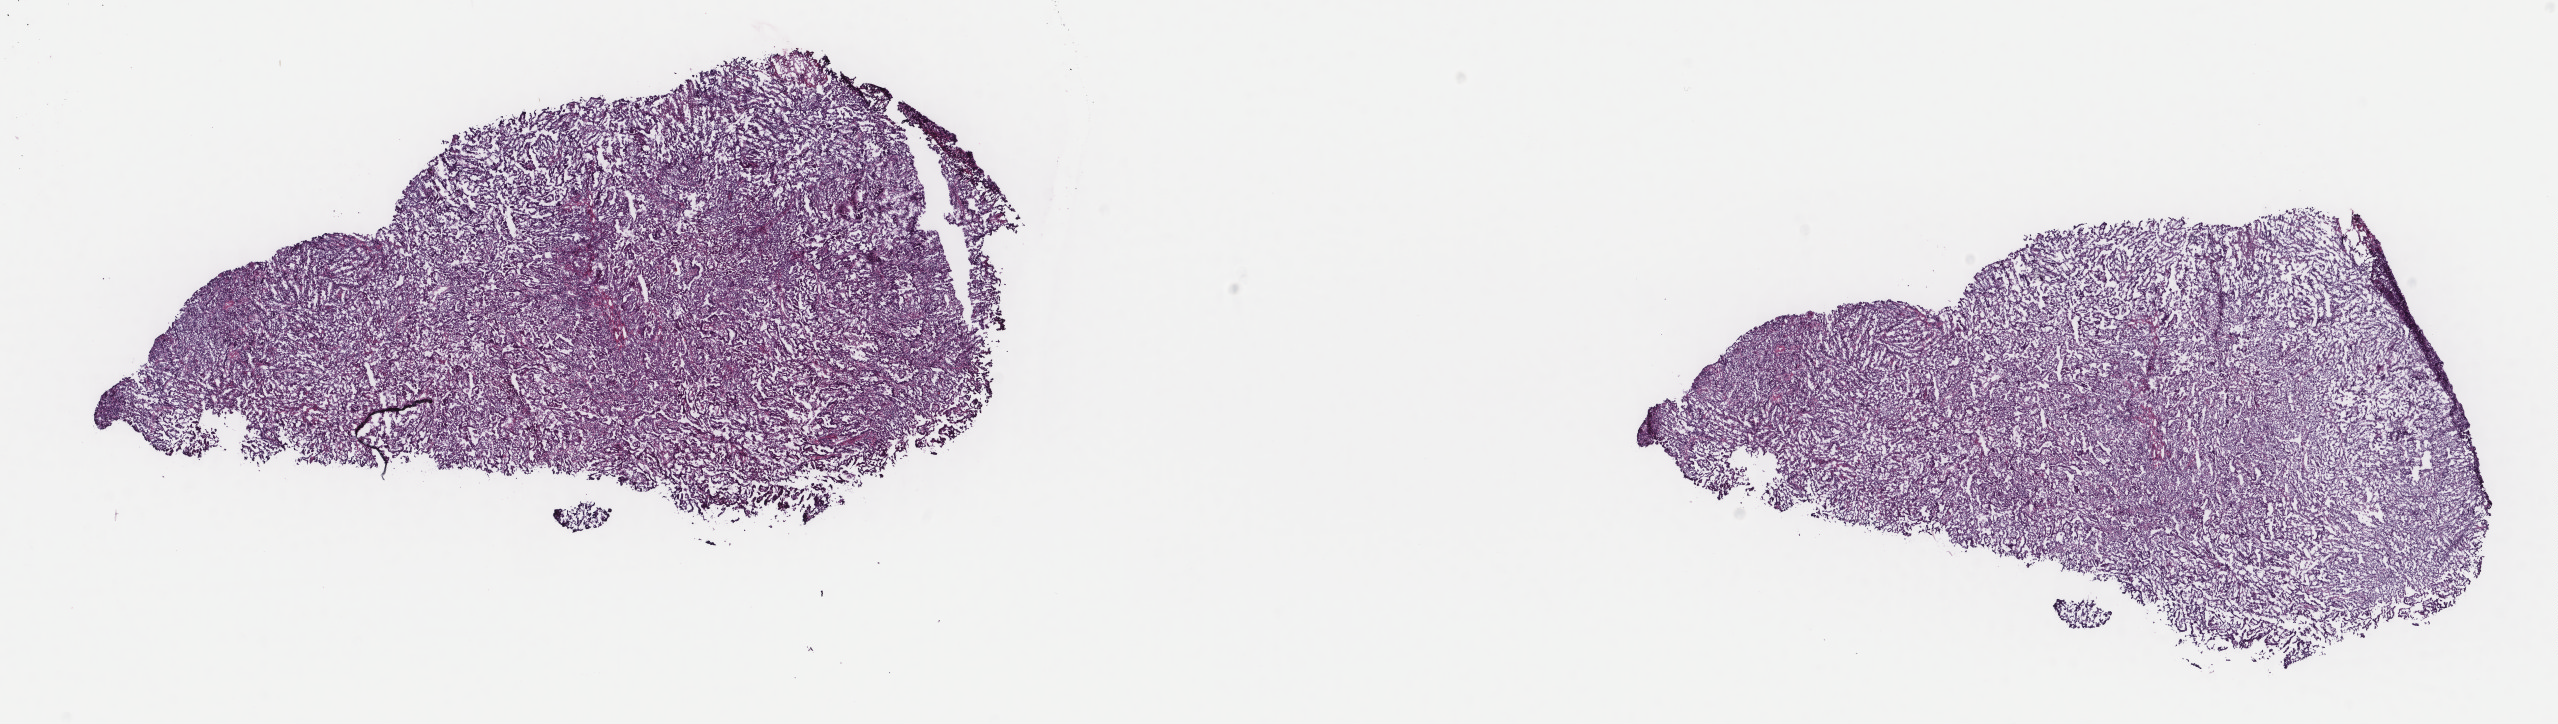
Whole-slide histology image, H&E, whole scanned area (about 20.3 x 5.7 mm) shown as a low-resolution overview. Frozen section from the top of the tissue portion. Primary tumour sample from the uterus. Female, age 45 years at initial diagnosis. Histologic grade: high grade. Composition of this section per pathologist review: tumour cells 100%, tumour nuclei 70%, normal cells 0%, stromal cells 0%, necrosis 0%. Inflammatory infiltration, as recorded: lymphocyte infiltration 0%, monocyte infiltration 0%, neutrophil infiltration 0%.
• diagnosis: Serous cystadenocarcinoma, NOS (endometrium)
• FIGO stage: IA